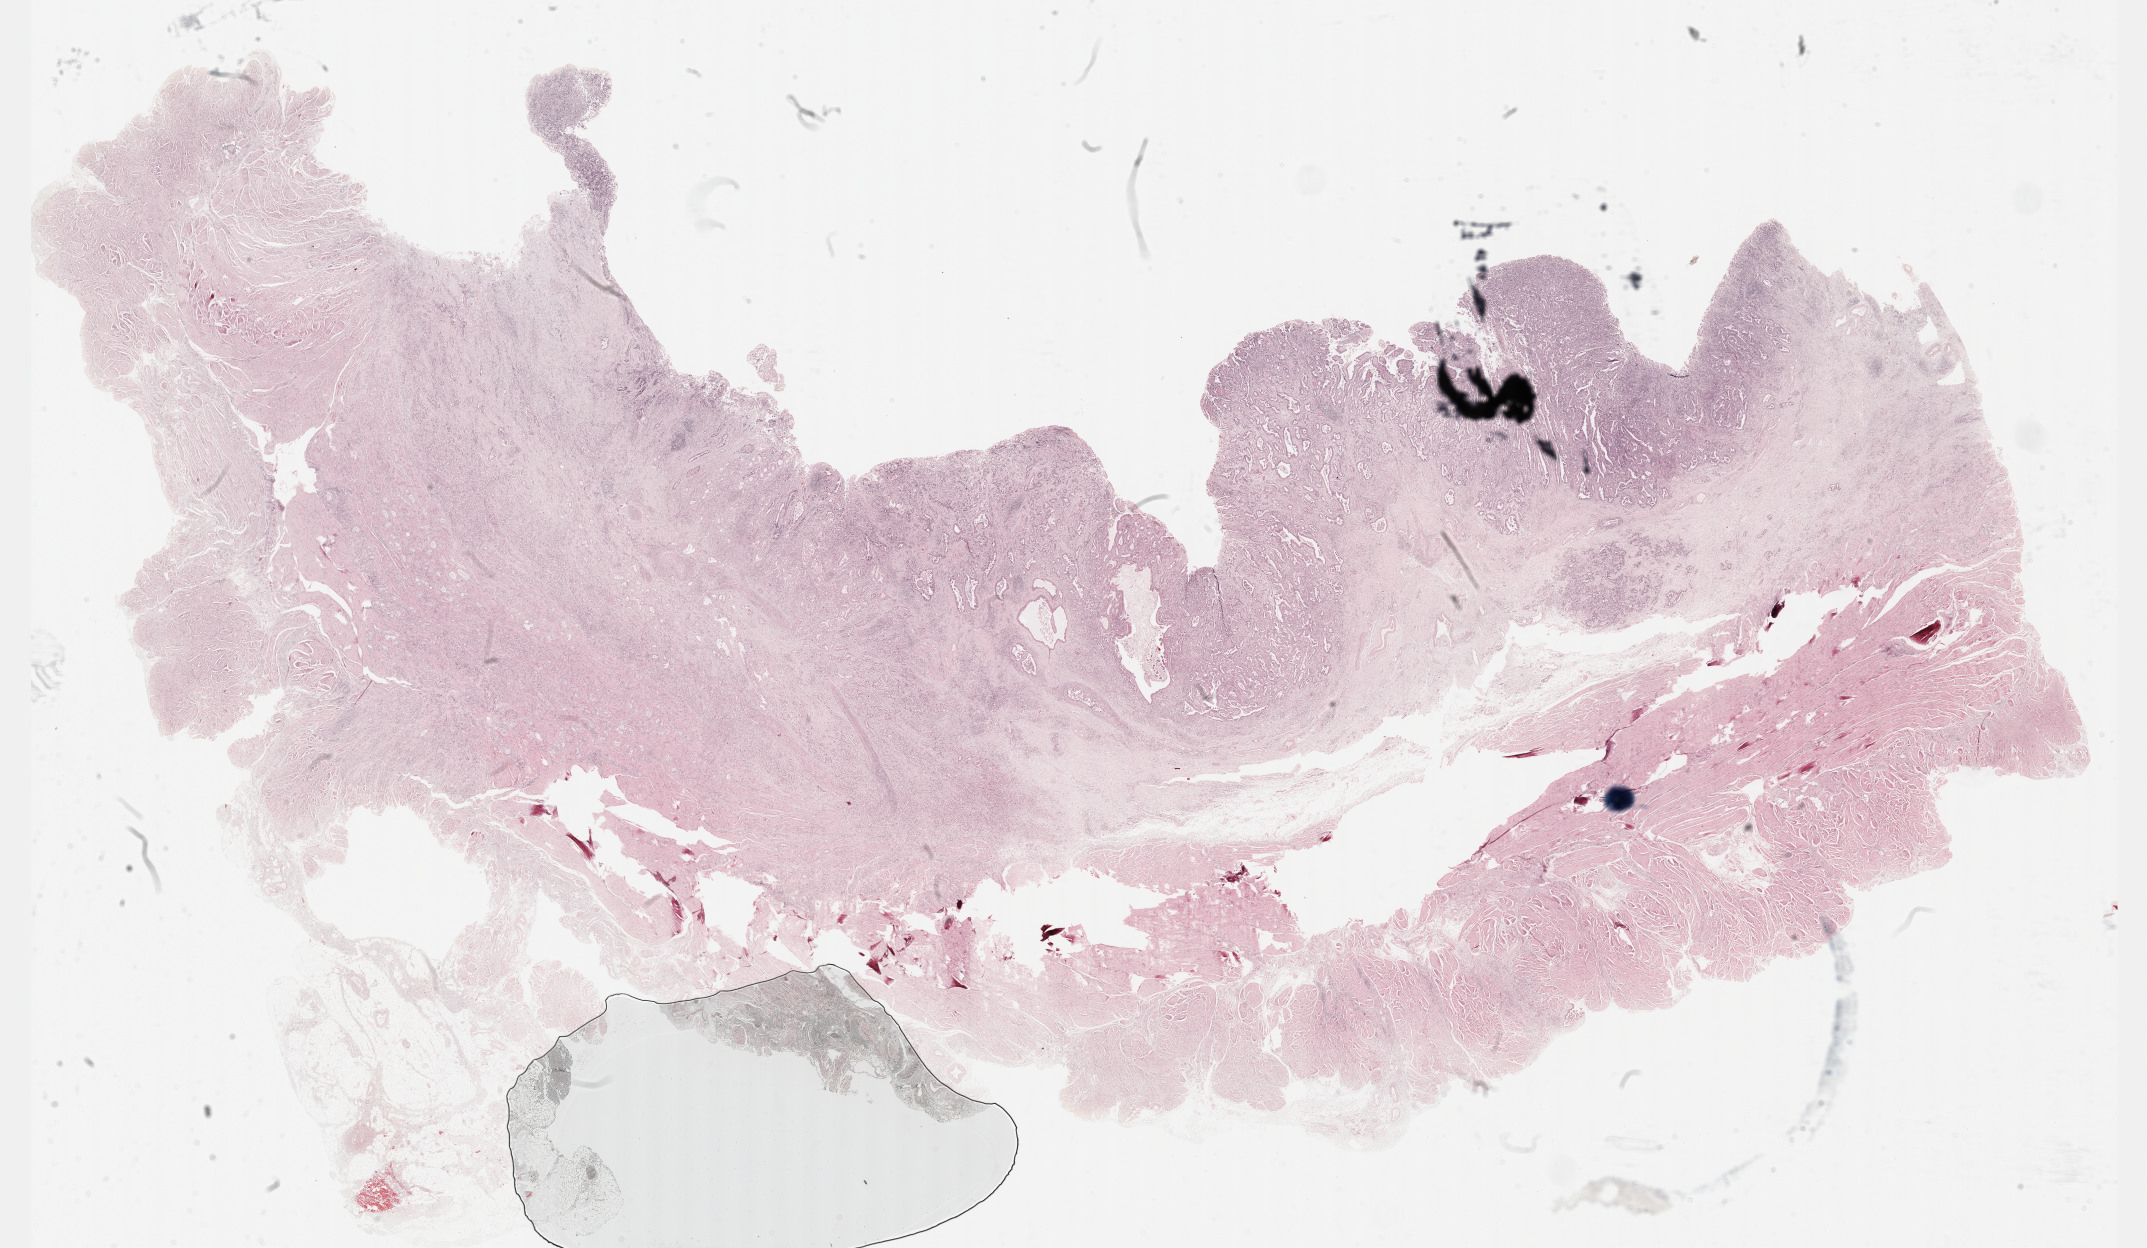
Whole-slide histology image, Hematoxylin and eosin (H&E) stained, shown as a low-resolution overview of the whole scanned area (about 34.7 x 20.2 mm). Formalin-fixed paraffin-embedded (FFPE) diagnostic section. Primary tumour sample from the esophagus. Male patient; age at initial diagnosis 80 years. Histologic grade: G2 (moderately differentiated).
Histologic diagnosis: Adenocarcinoma, NOS (lower third of esophagus). AJCC pathologic stage: IIA.